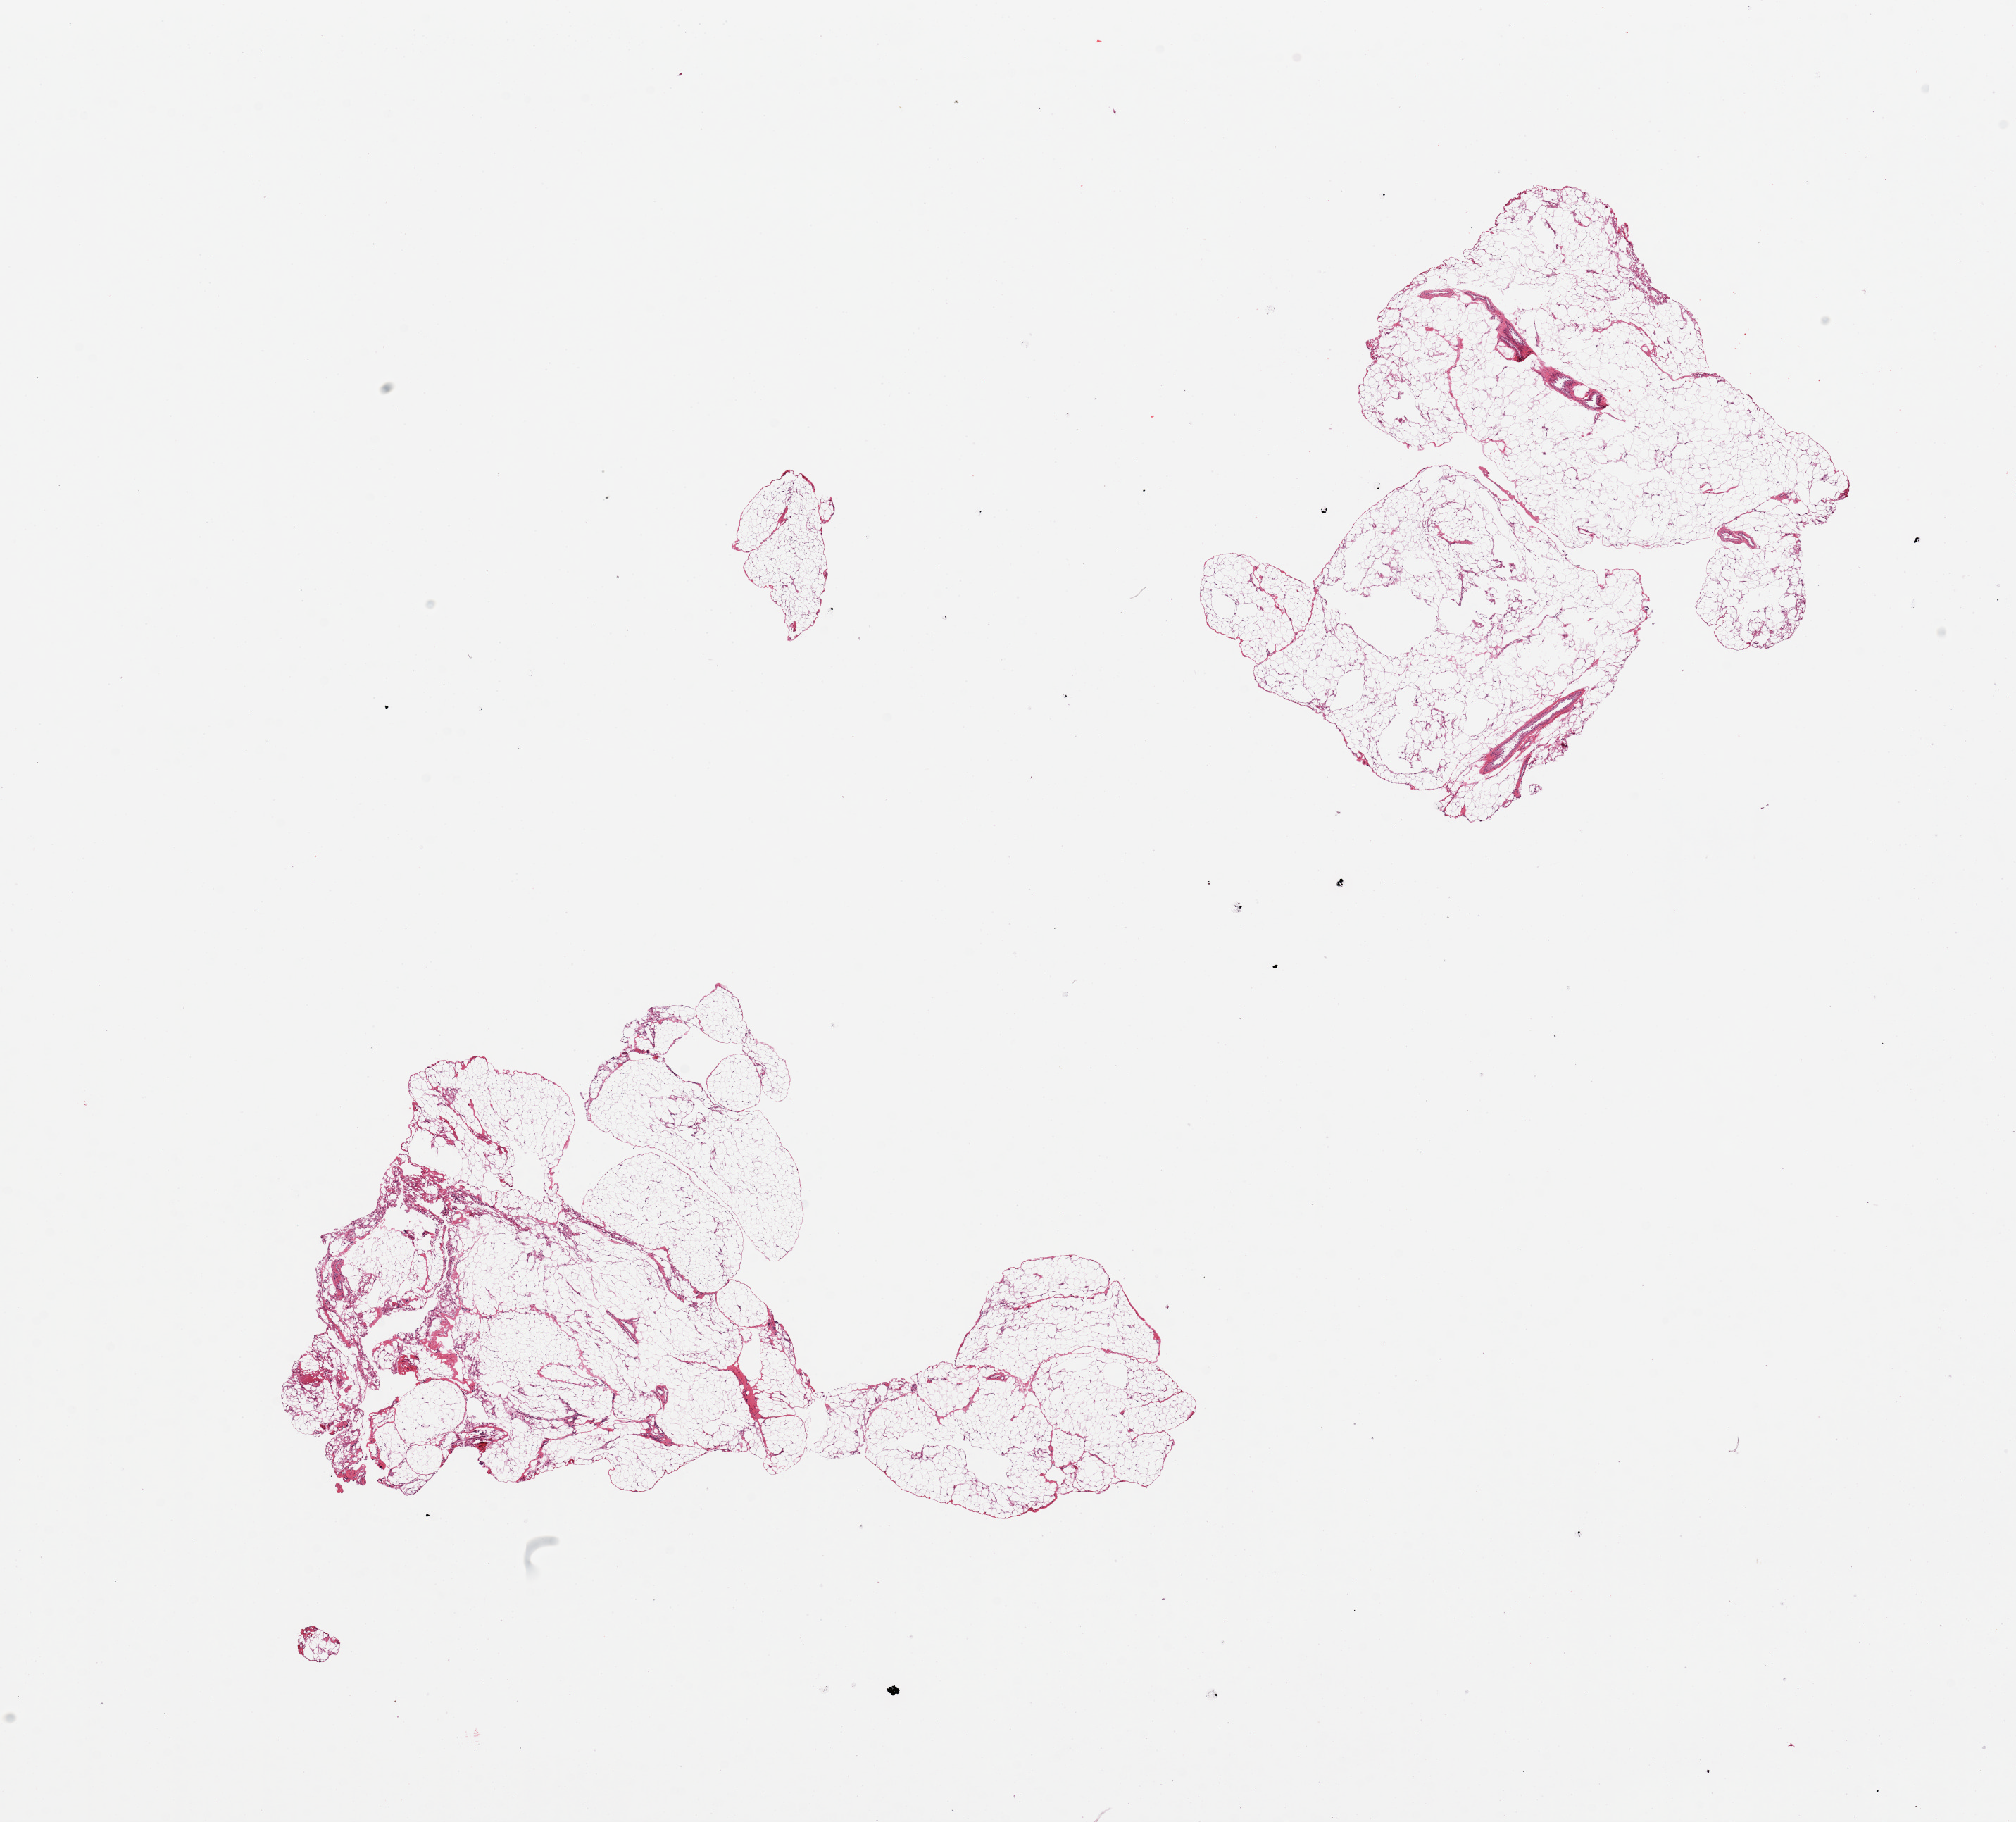
H&E whole-slide image, brightfield, a low-resolution overview of the entire scanned area, about 22.6 x 20.5 mm; PAXgene-fixed paraffin-embedded (PFPE) section; target tissue: omentum; tissue donor sample. Female donor.
• review note (as recorded): 2 pieces